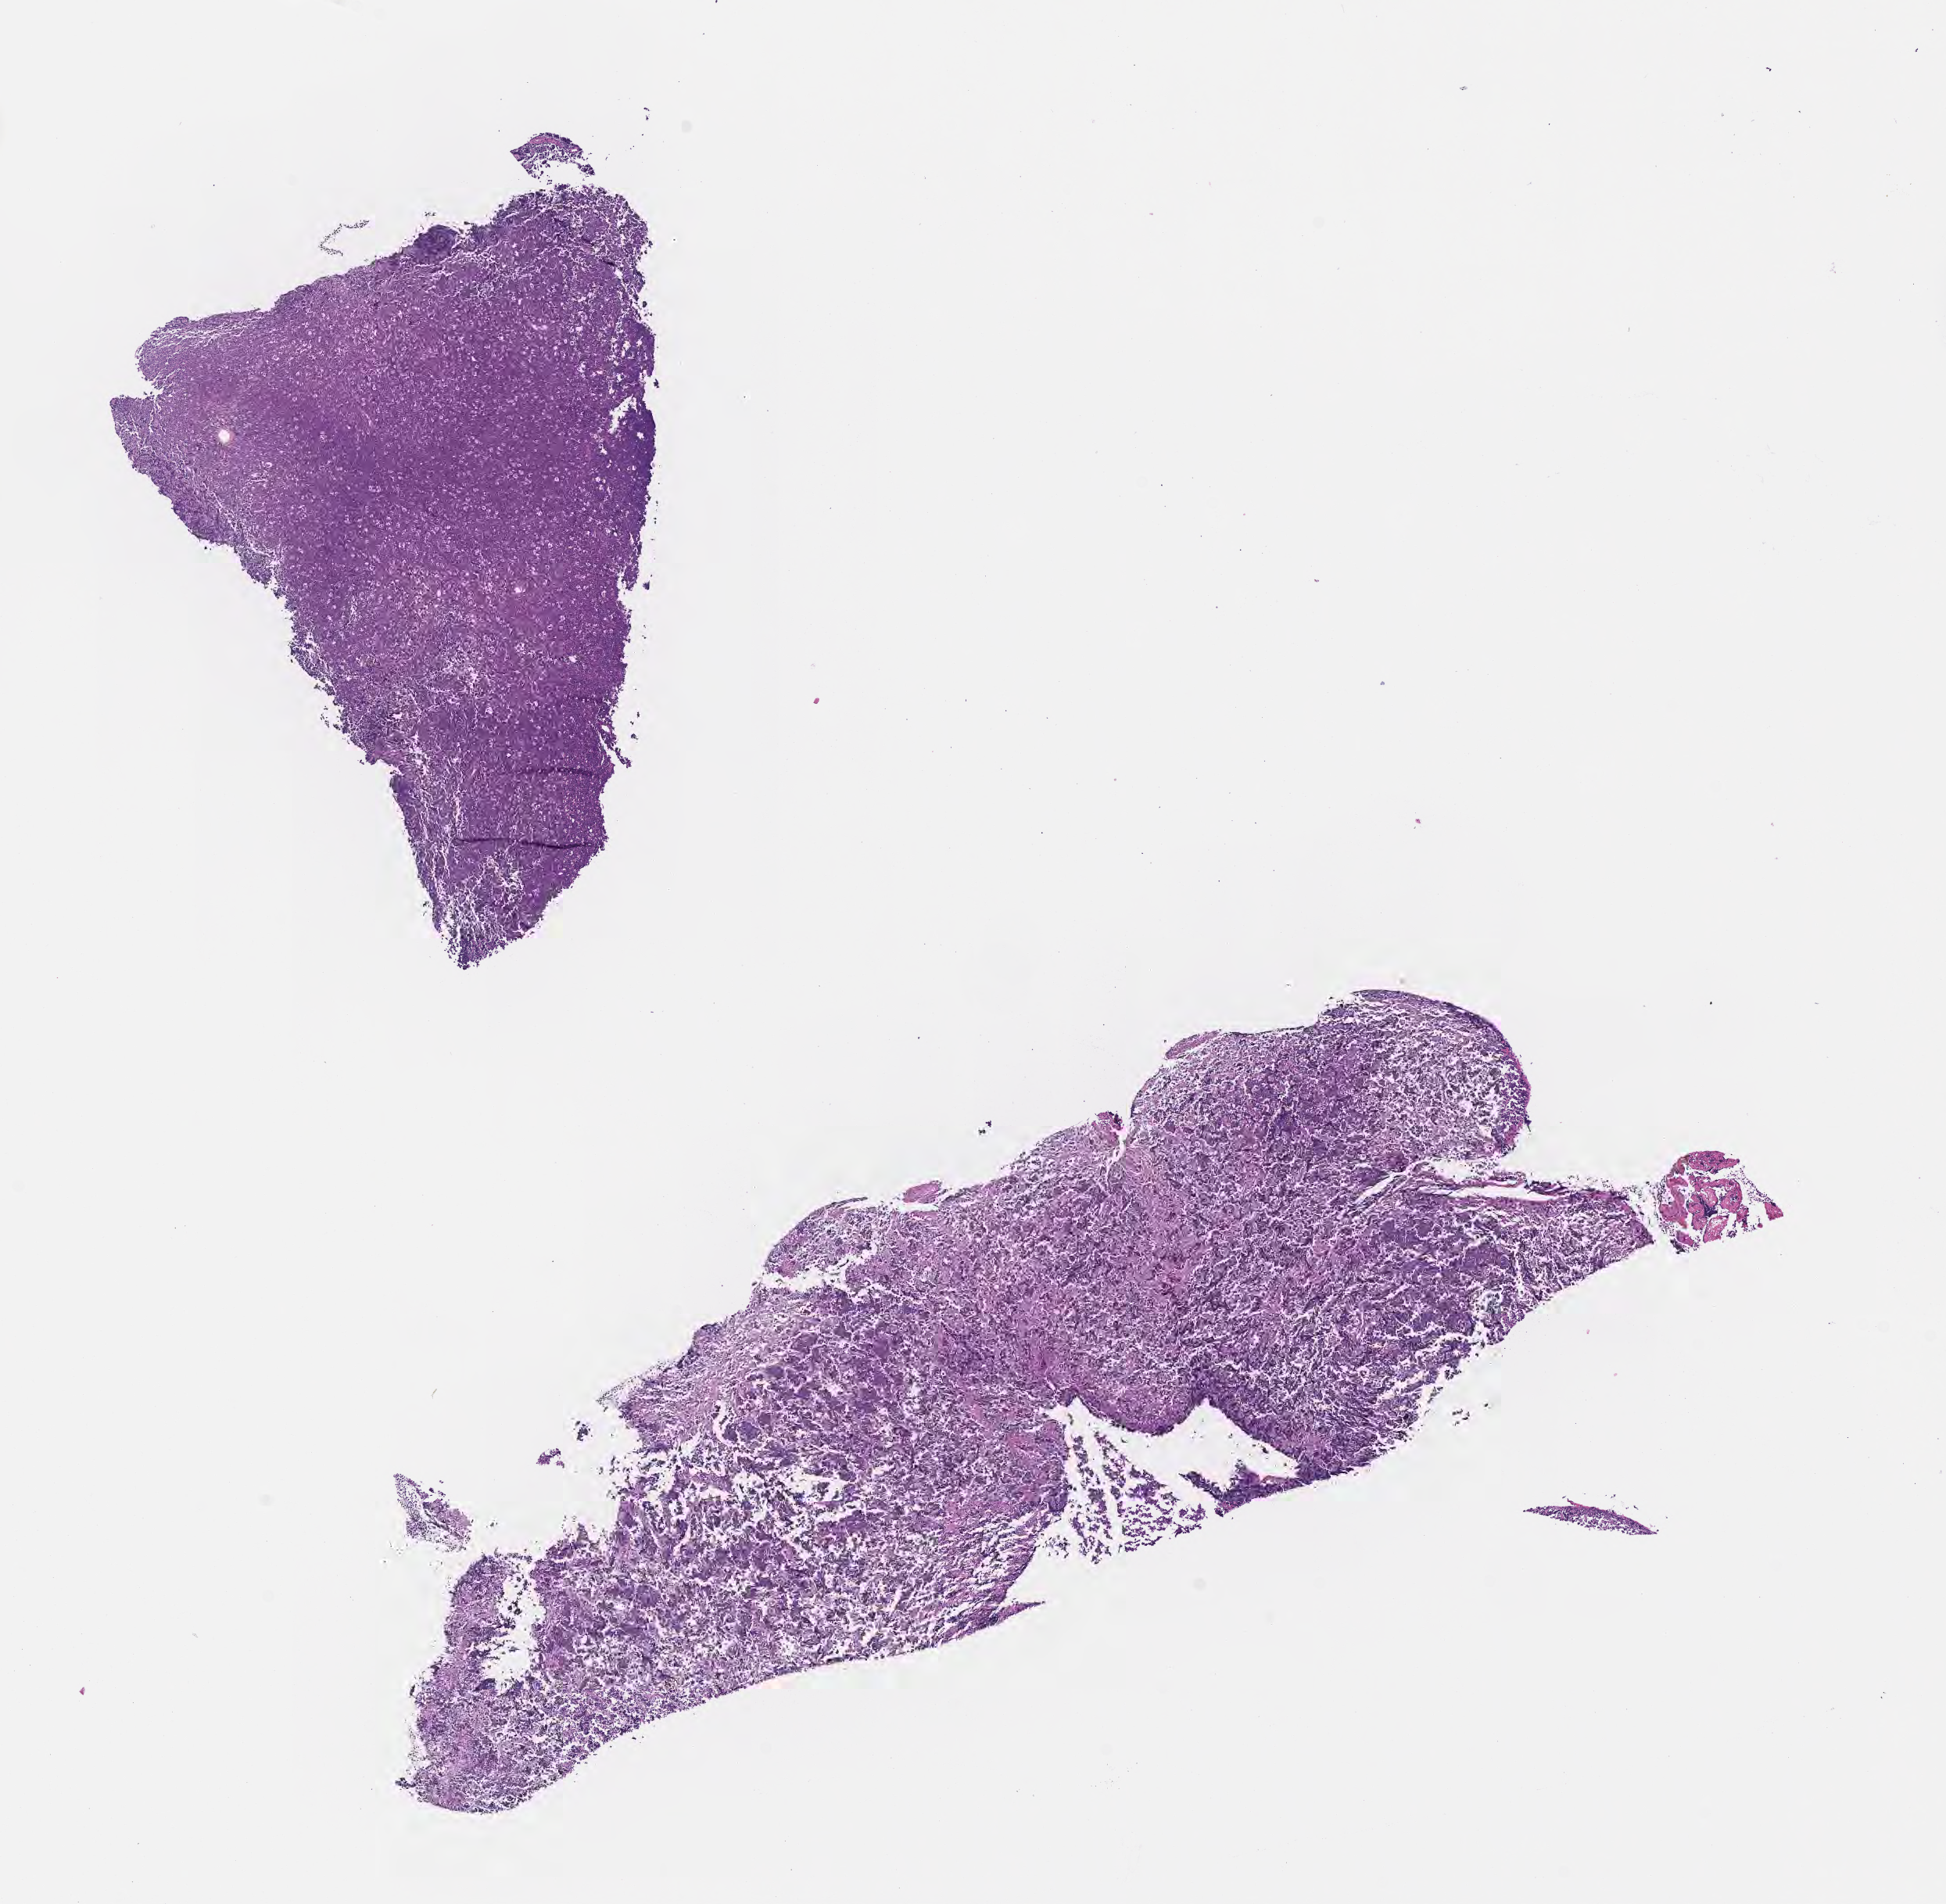
Digitized hematoxylin and eosin (H&E)-stained section, a low-resolution overview of the entire scanned area, about 10.1 x 9.8 mm. Specimen: tumor tissue. Male, age 2 years at initial diagnosis.
Diagnosis: Burkitt lymphoma, NOS.